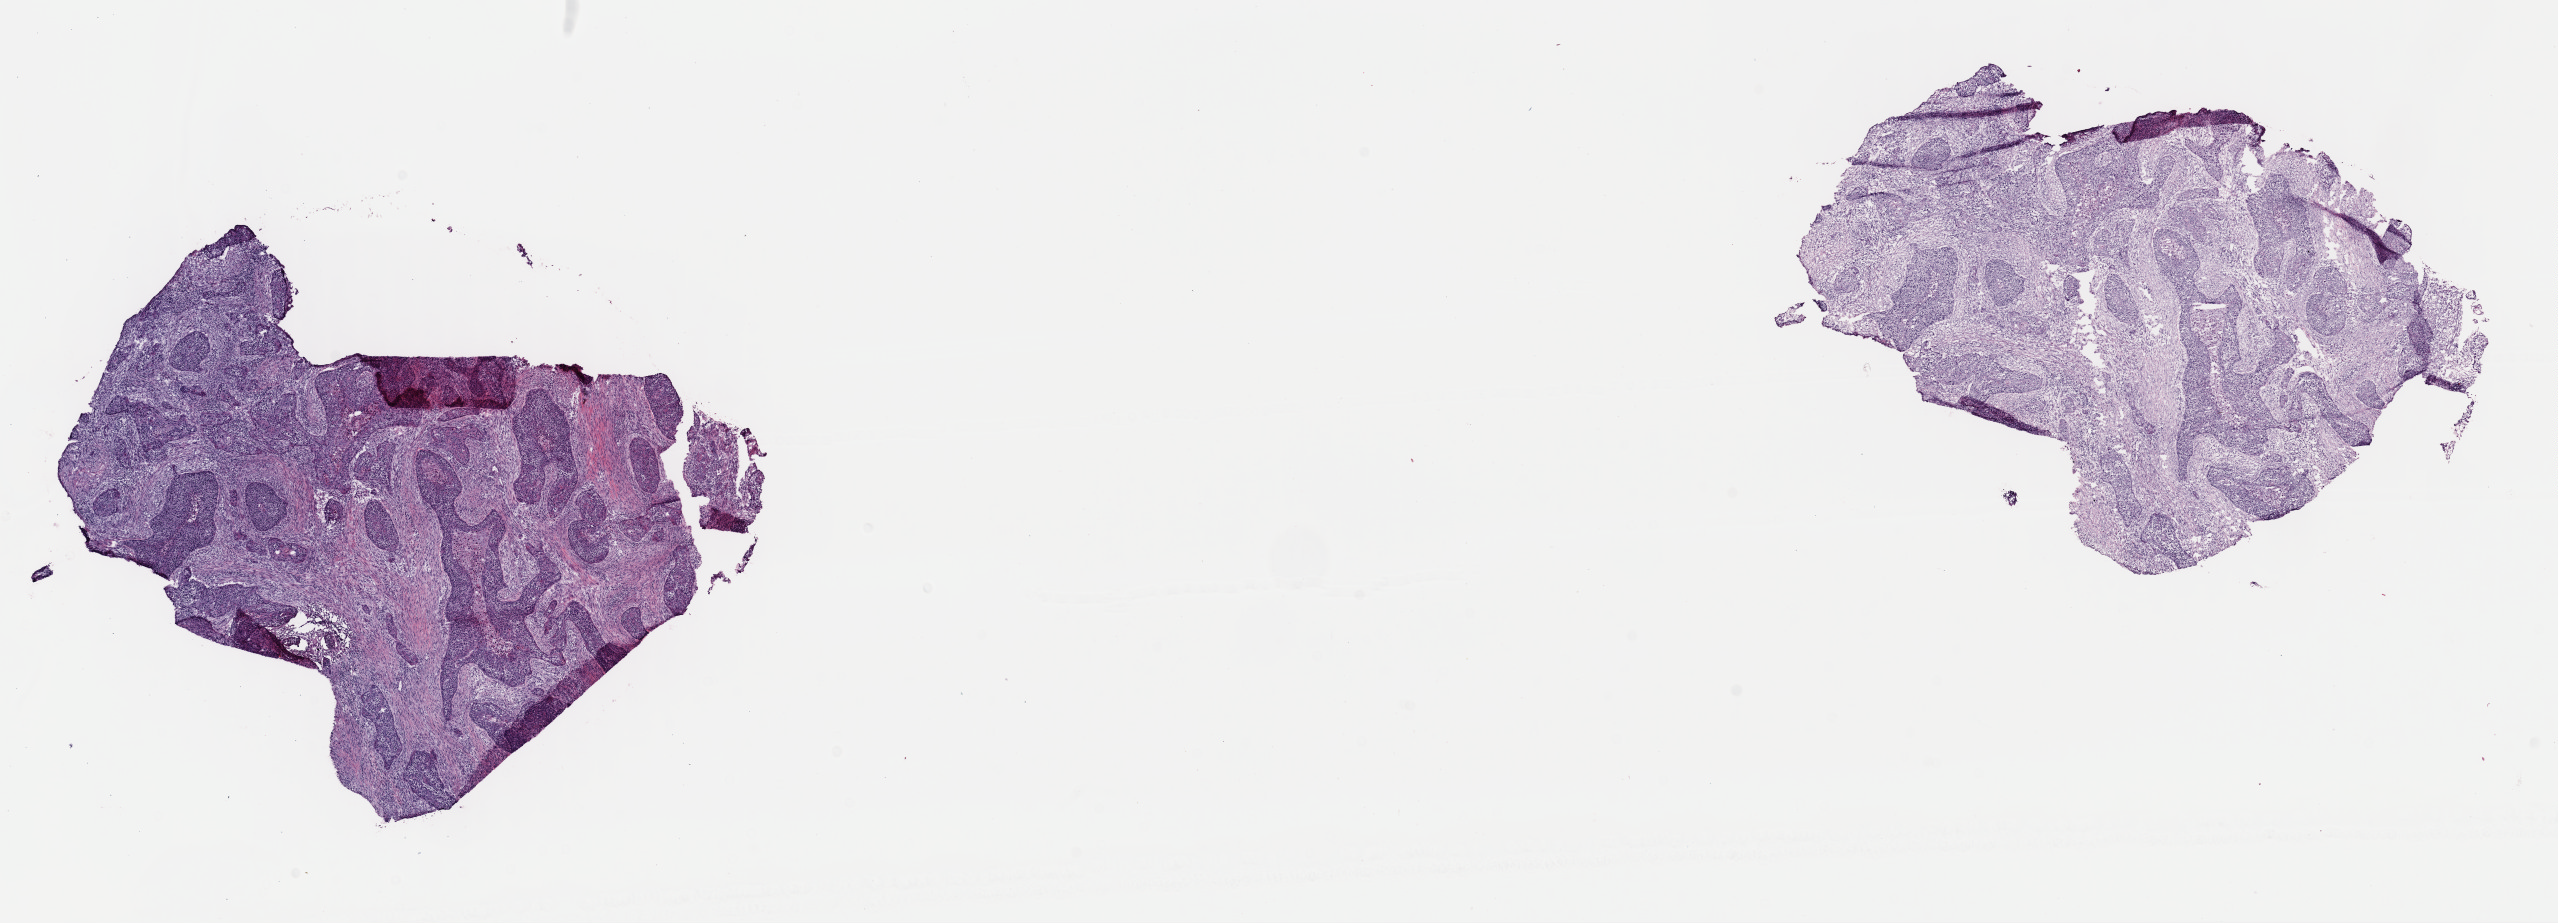
Digitized Hematoxylin and eosin (H&E) stained tissue section (whole slide), a low-resolution overview of the entire scanned area, about 20.2 x 7.3 mm, frozen section, cervix, primary tumour sample. Female, age 53 years at initial diagnosis. Histologic grade: G1 (well differentiated). Slide review estimates, as recorded: tumour cells 70%, tumour nuclei 70%, normal cells 0%, stromal cells 25%, necrosis 5%. Infiltration values recorded for this section: lymphocyte infiltration 60%, monocyte infiltration 10%, neutrophil infiltration 20%.
Histologic diagnosis: Squamous cell carcinoma, keratinizing, NOS (cervix uteri). FIGO stage: IIA. Lymph nodes positive (case pathology): 0 of 8 examined.